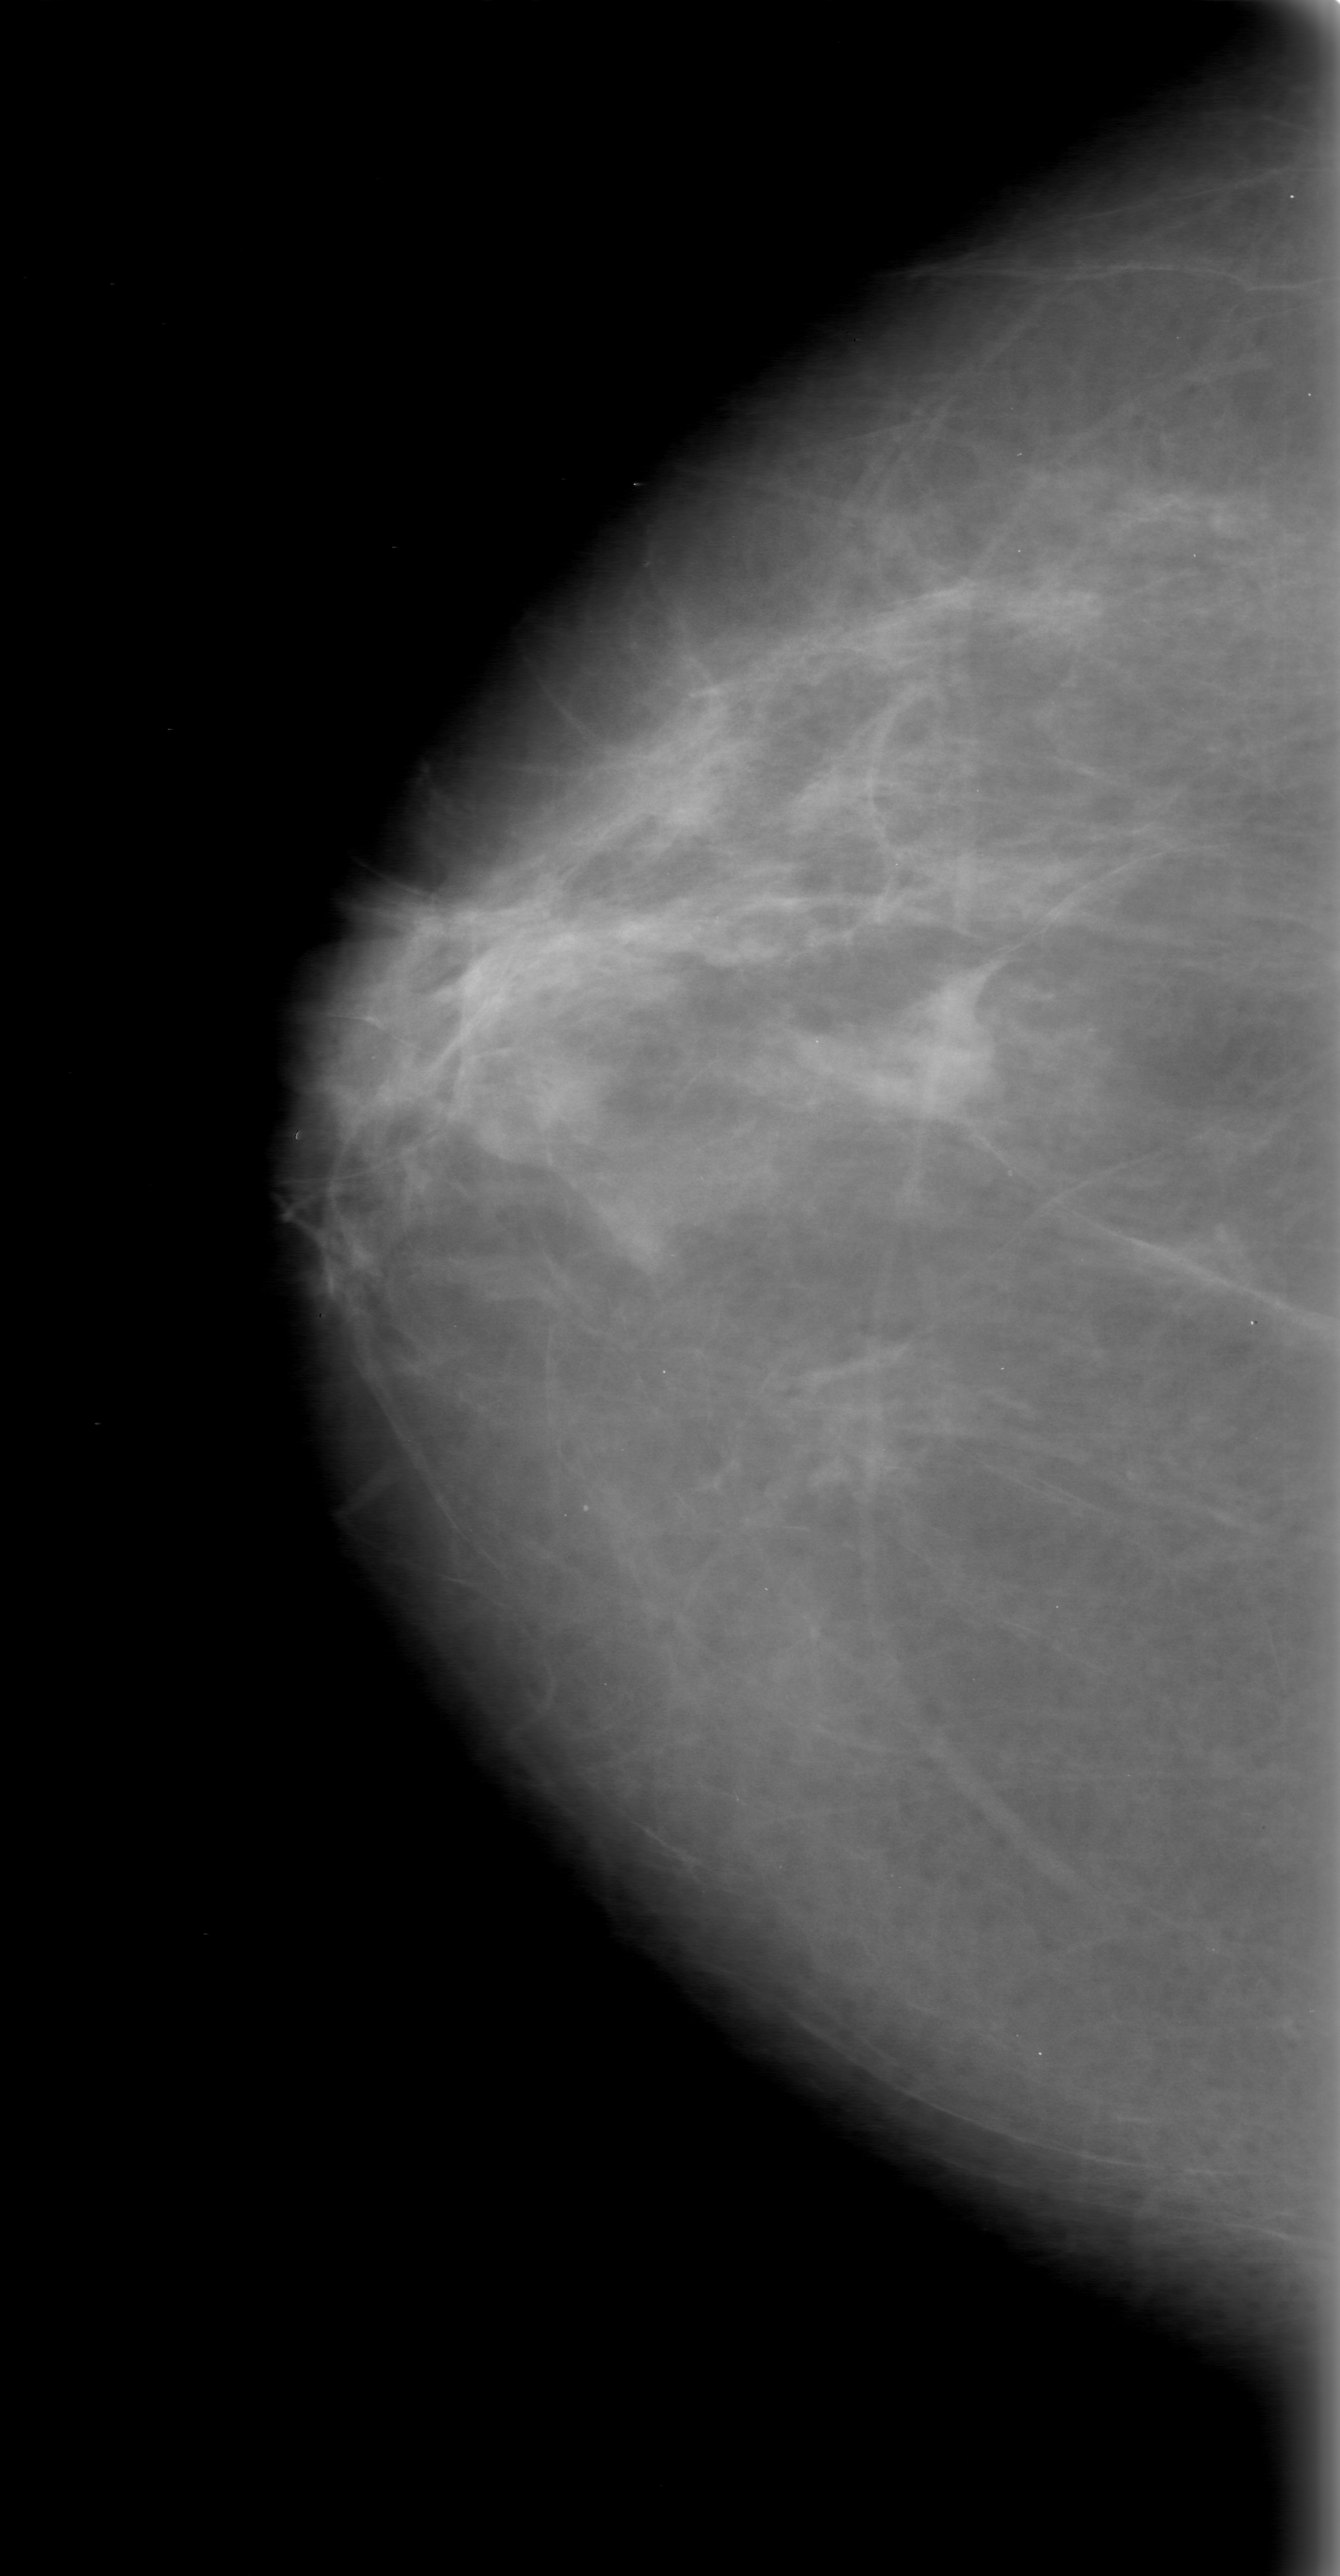
Digitized screen-film mammogram; right breast; CC view; breast composition: scattered fibroglandular densities (BI-RADS density category 2 of 4); 1340 × 2576 image matrix.
Expert-marked regions of interest on this film, with their recorded descriptors:
- mass, shape irregular, margins obscured; BI-RADS assessment category 0 (incomplete: needs additional imaging); subtlety rating 5 on a 1 (subtle) to 5 (obvious) scale; pathology (as recorded): benign: bounding box [x1, y1, x2, y2] px = [824, 963, 1013, 1155]